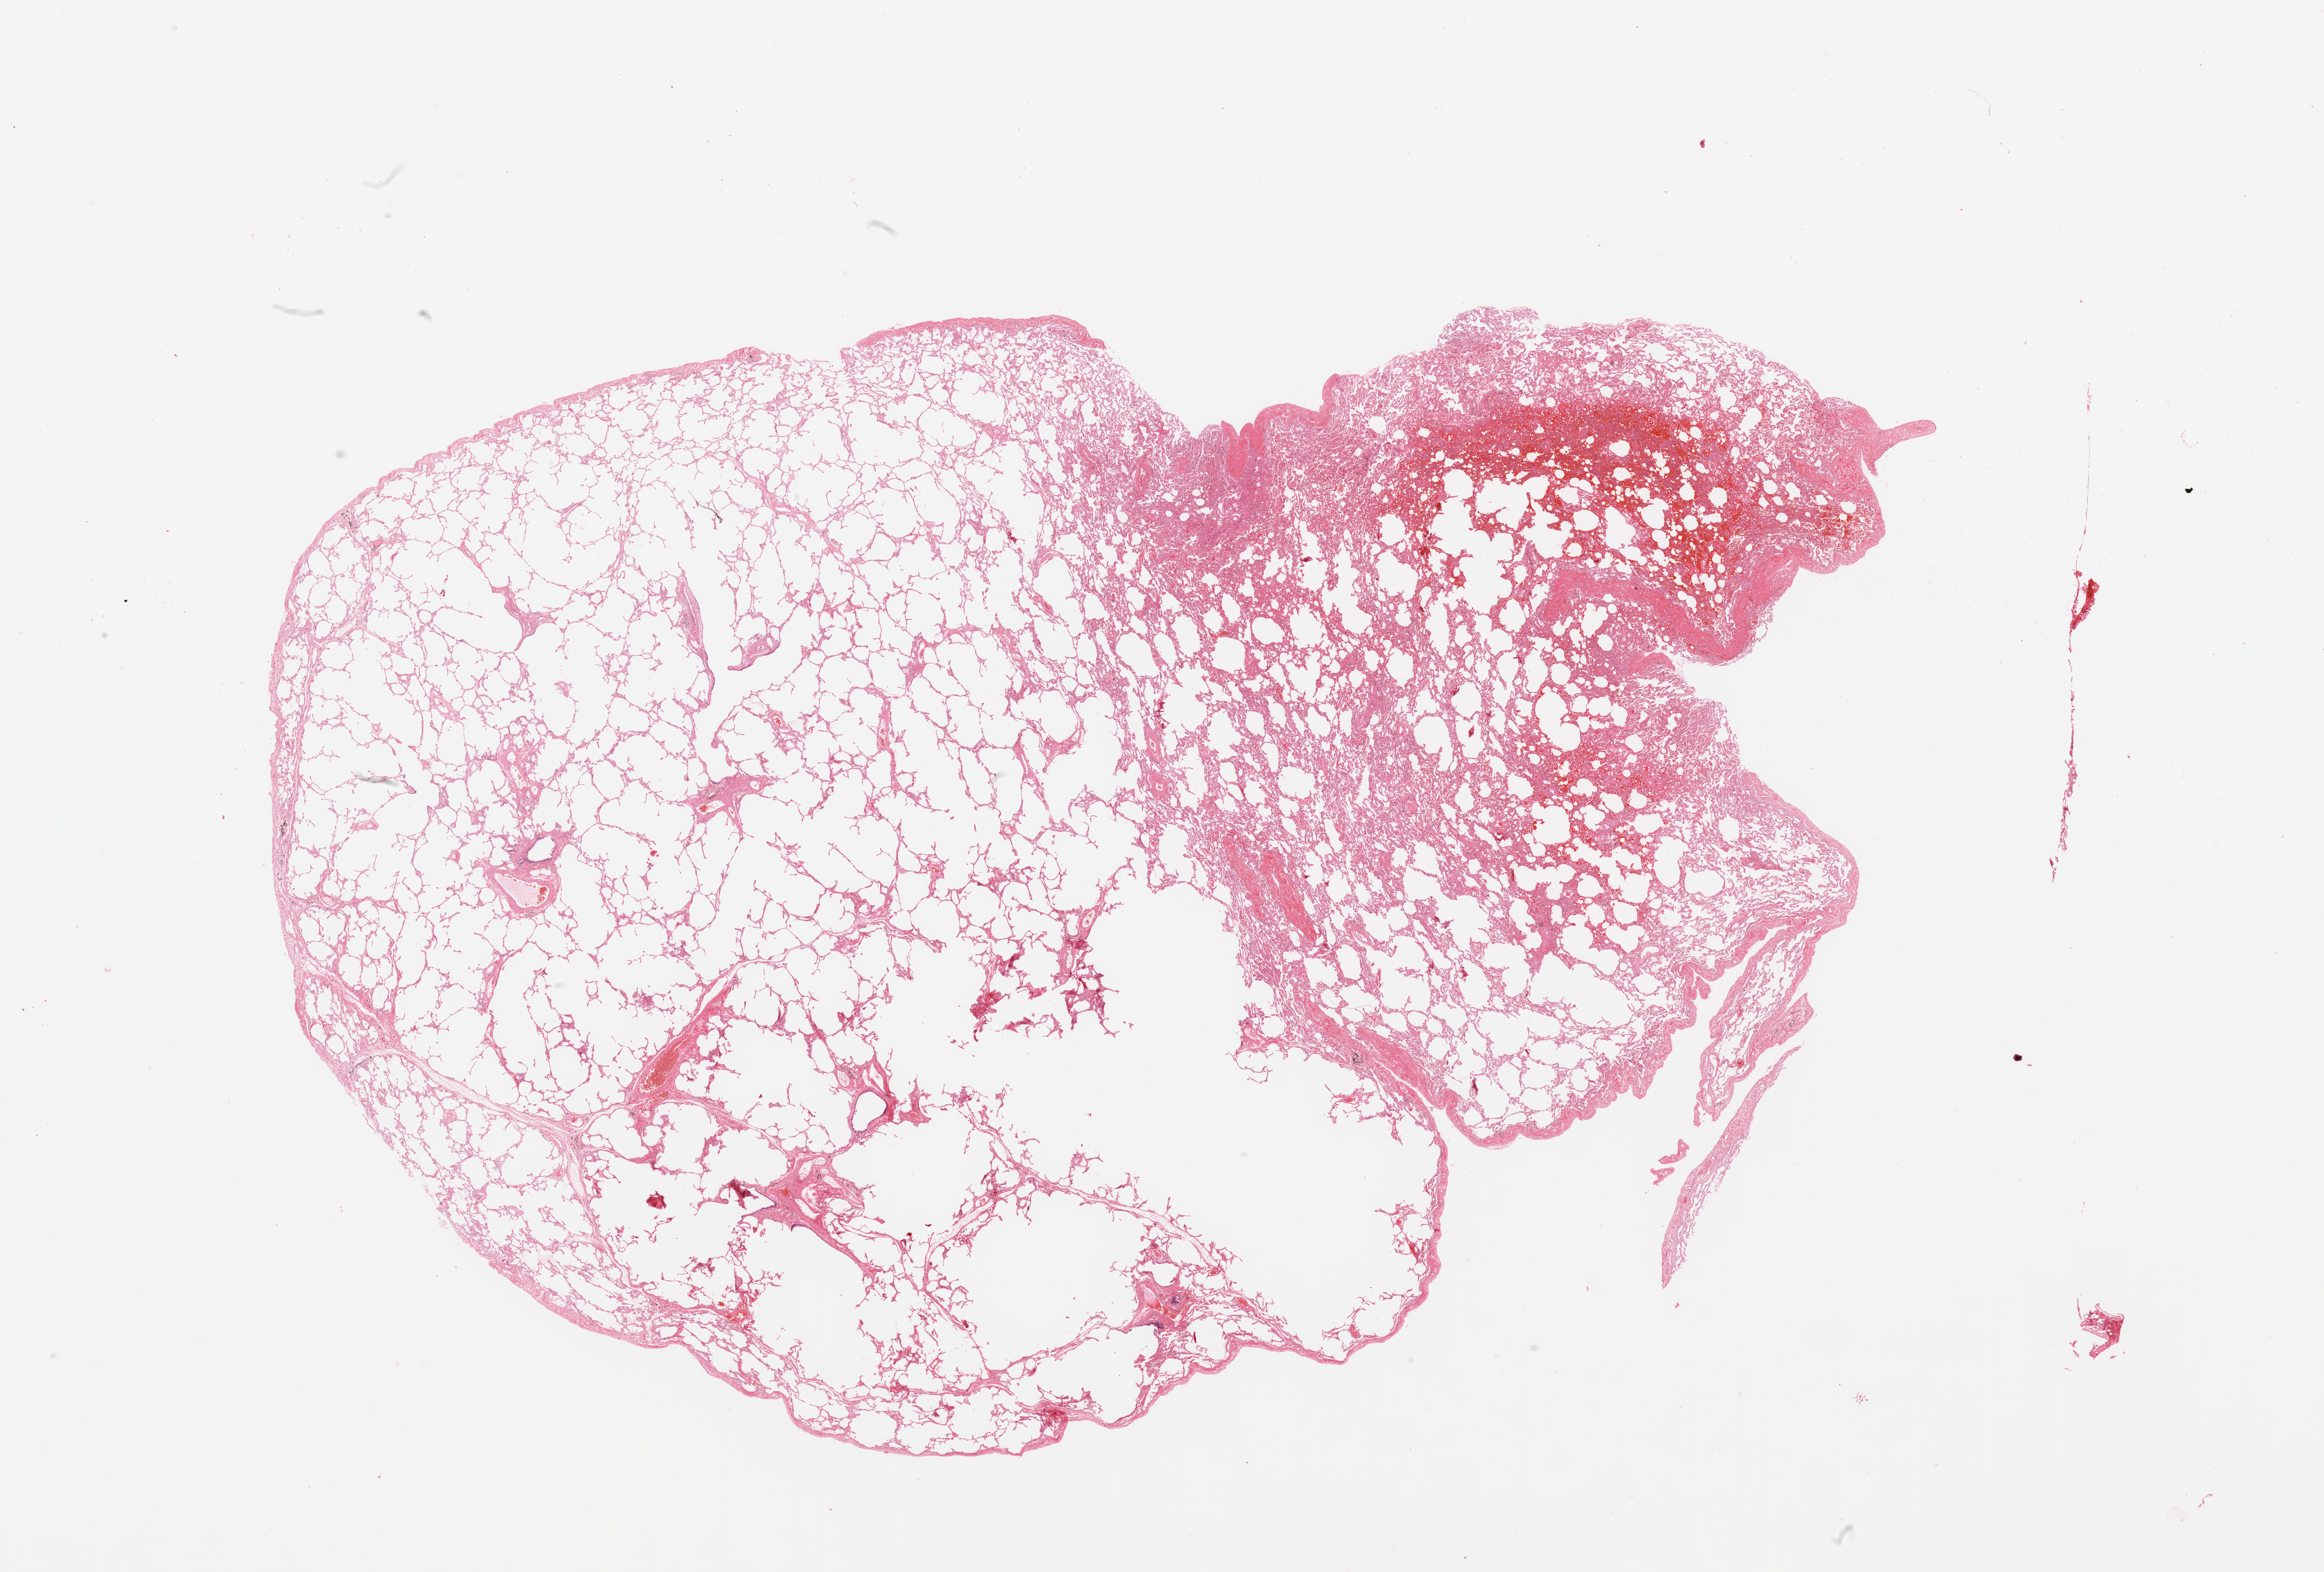
Digitized Hematoxylin and eosin (H&E) stained tissue section (whole slide), a low-resolution overview of the entire scanned area, about 31.5 x 21.3 mm; normal (non-tumour) tissue sample, lung. 69-year-old female patient.
This section: normal (non-tumour) tissue from the same patient. Patient diagnosis: Adenocarcinoma, NOS.